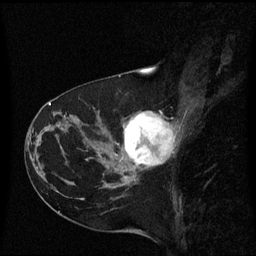
Breast MRI (dynamic contrast-enhanced), one sagittal slice. Slice 27 of 60 in the series (ordered by position). Dynamic contrast-enhanced series, image 2 of 3 at this slice position (ordered by acquisition). 1.5 T. TE 4.2 ms, TR 8.4 ms. 2 mm slice thickness. 256 × 256 image matrix, field of view 220 × 220 mm. Female patient, age 41 years. From the clinical record (not read from this slice): setting: breast cancer imaged before/during neoadjuvant chemotherapy; receptor status: triple-negative.
Annotated regions visible in this slice (semi-automatic segmentation, software-assisted and operator-edited):
- analysis volume of interest (the breast-tissue region the enhancement analysis was run in; not a lesion): box from (x=116, y=112) to (x=177, y=177) px
- tumour enhancement mask (voxels above the 70 % enhancement threshold inside the analysis volume of interest): (x=124, y=112)–(x=172, y=169)